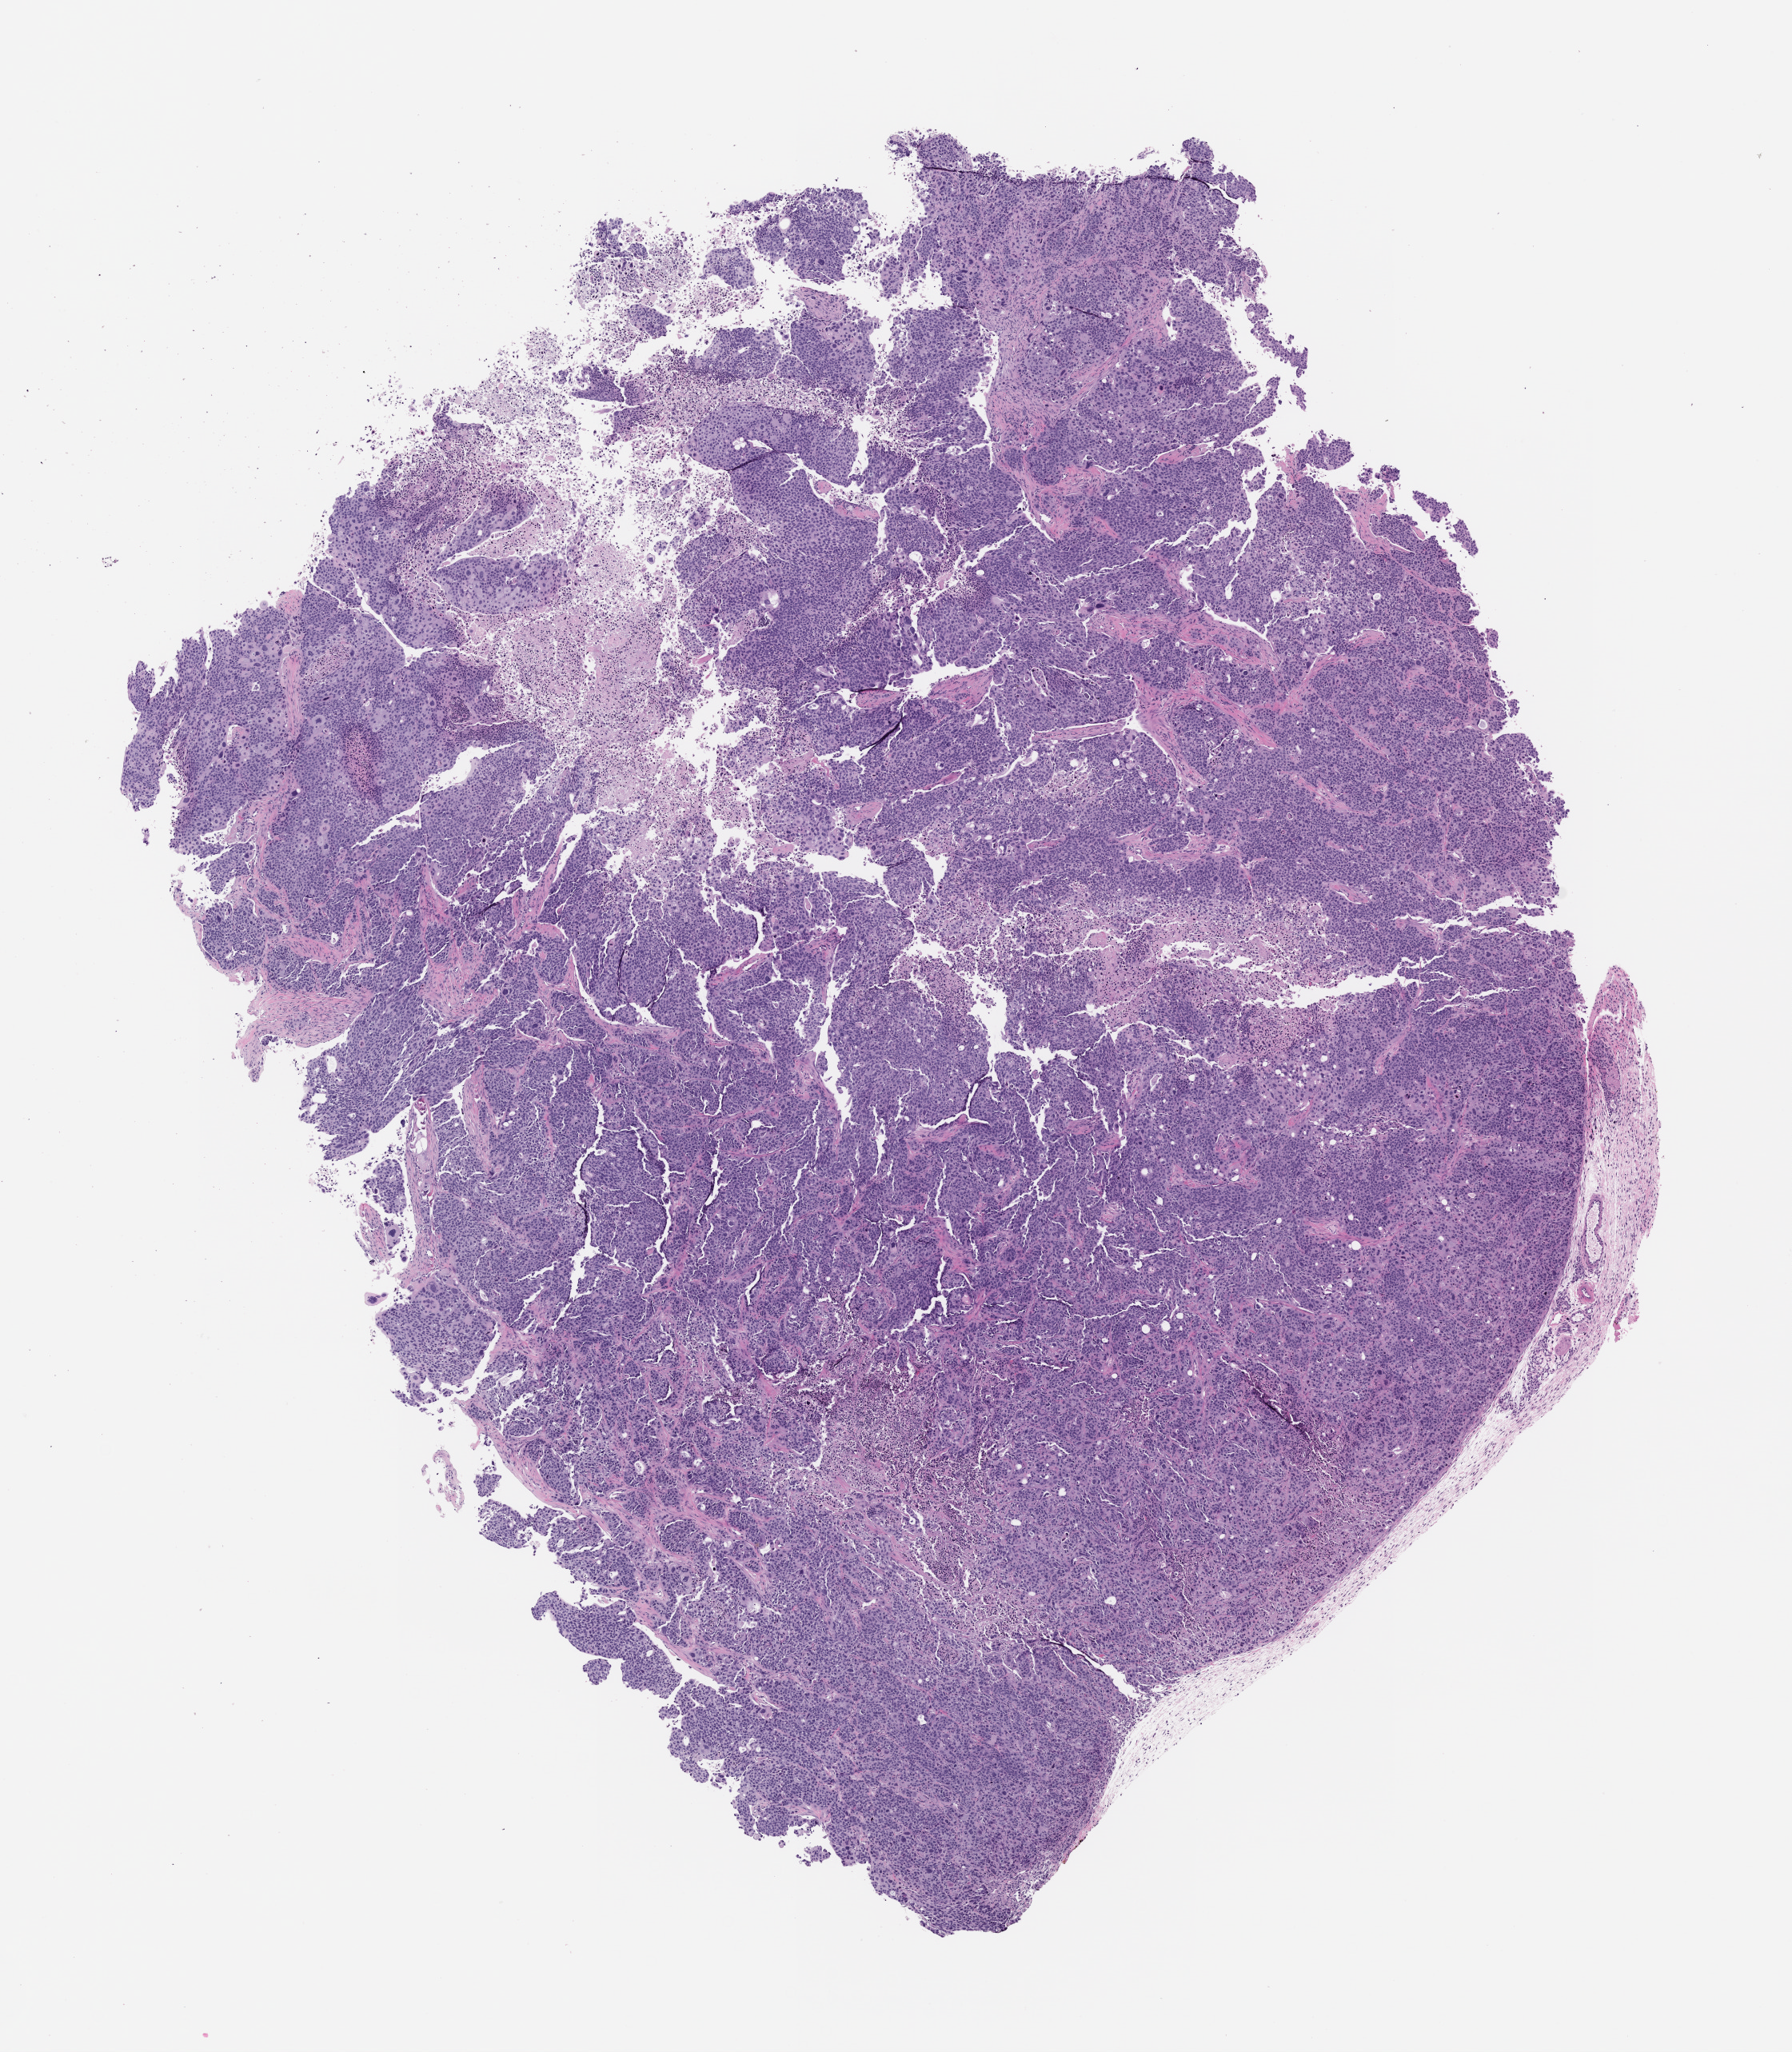
H&E whole-slide image of a patient-derived xenograft (PDX) tumor grown in a mouse, passage 3 — shown as a low-resolution overview of the whole scanned area (about 9.0 x 10.3 mm), formalin-fixed paraffin-embedded section, originating tumor site category: bladder.
Originating patient diagnosis: Urothelial Carcinoma.